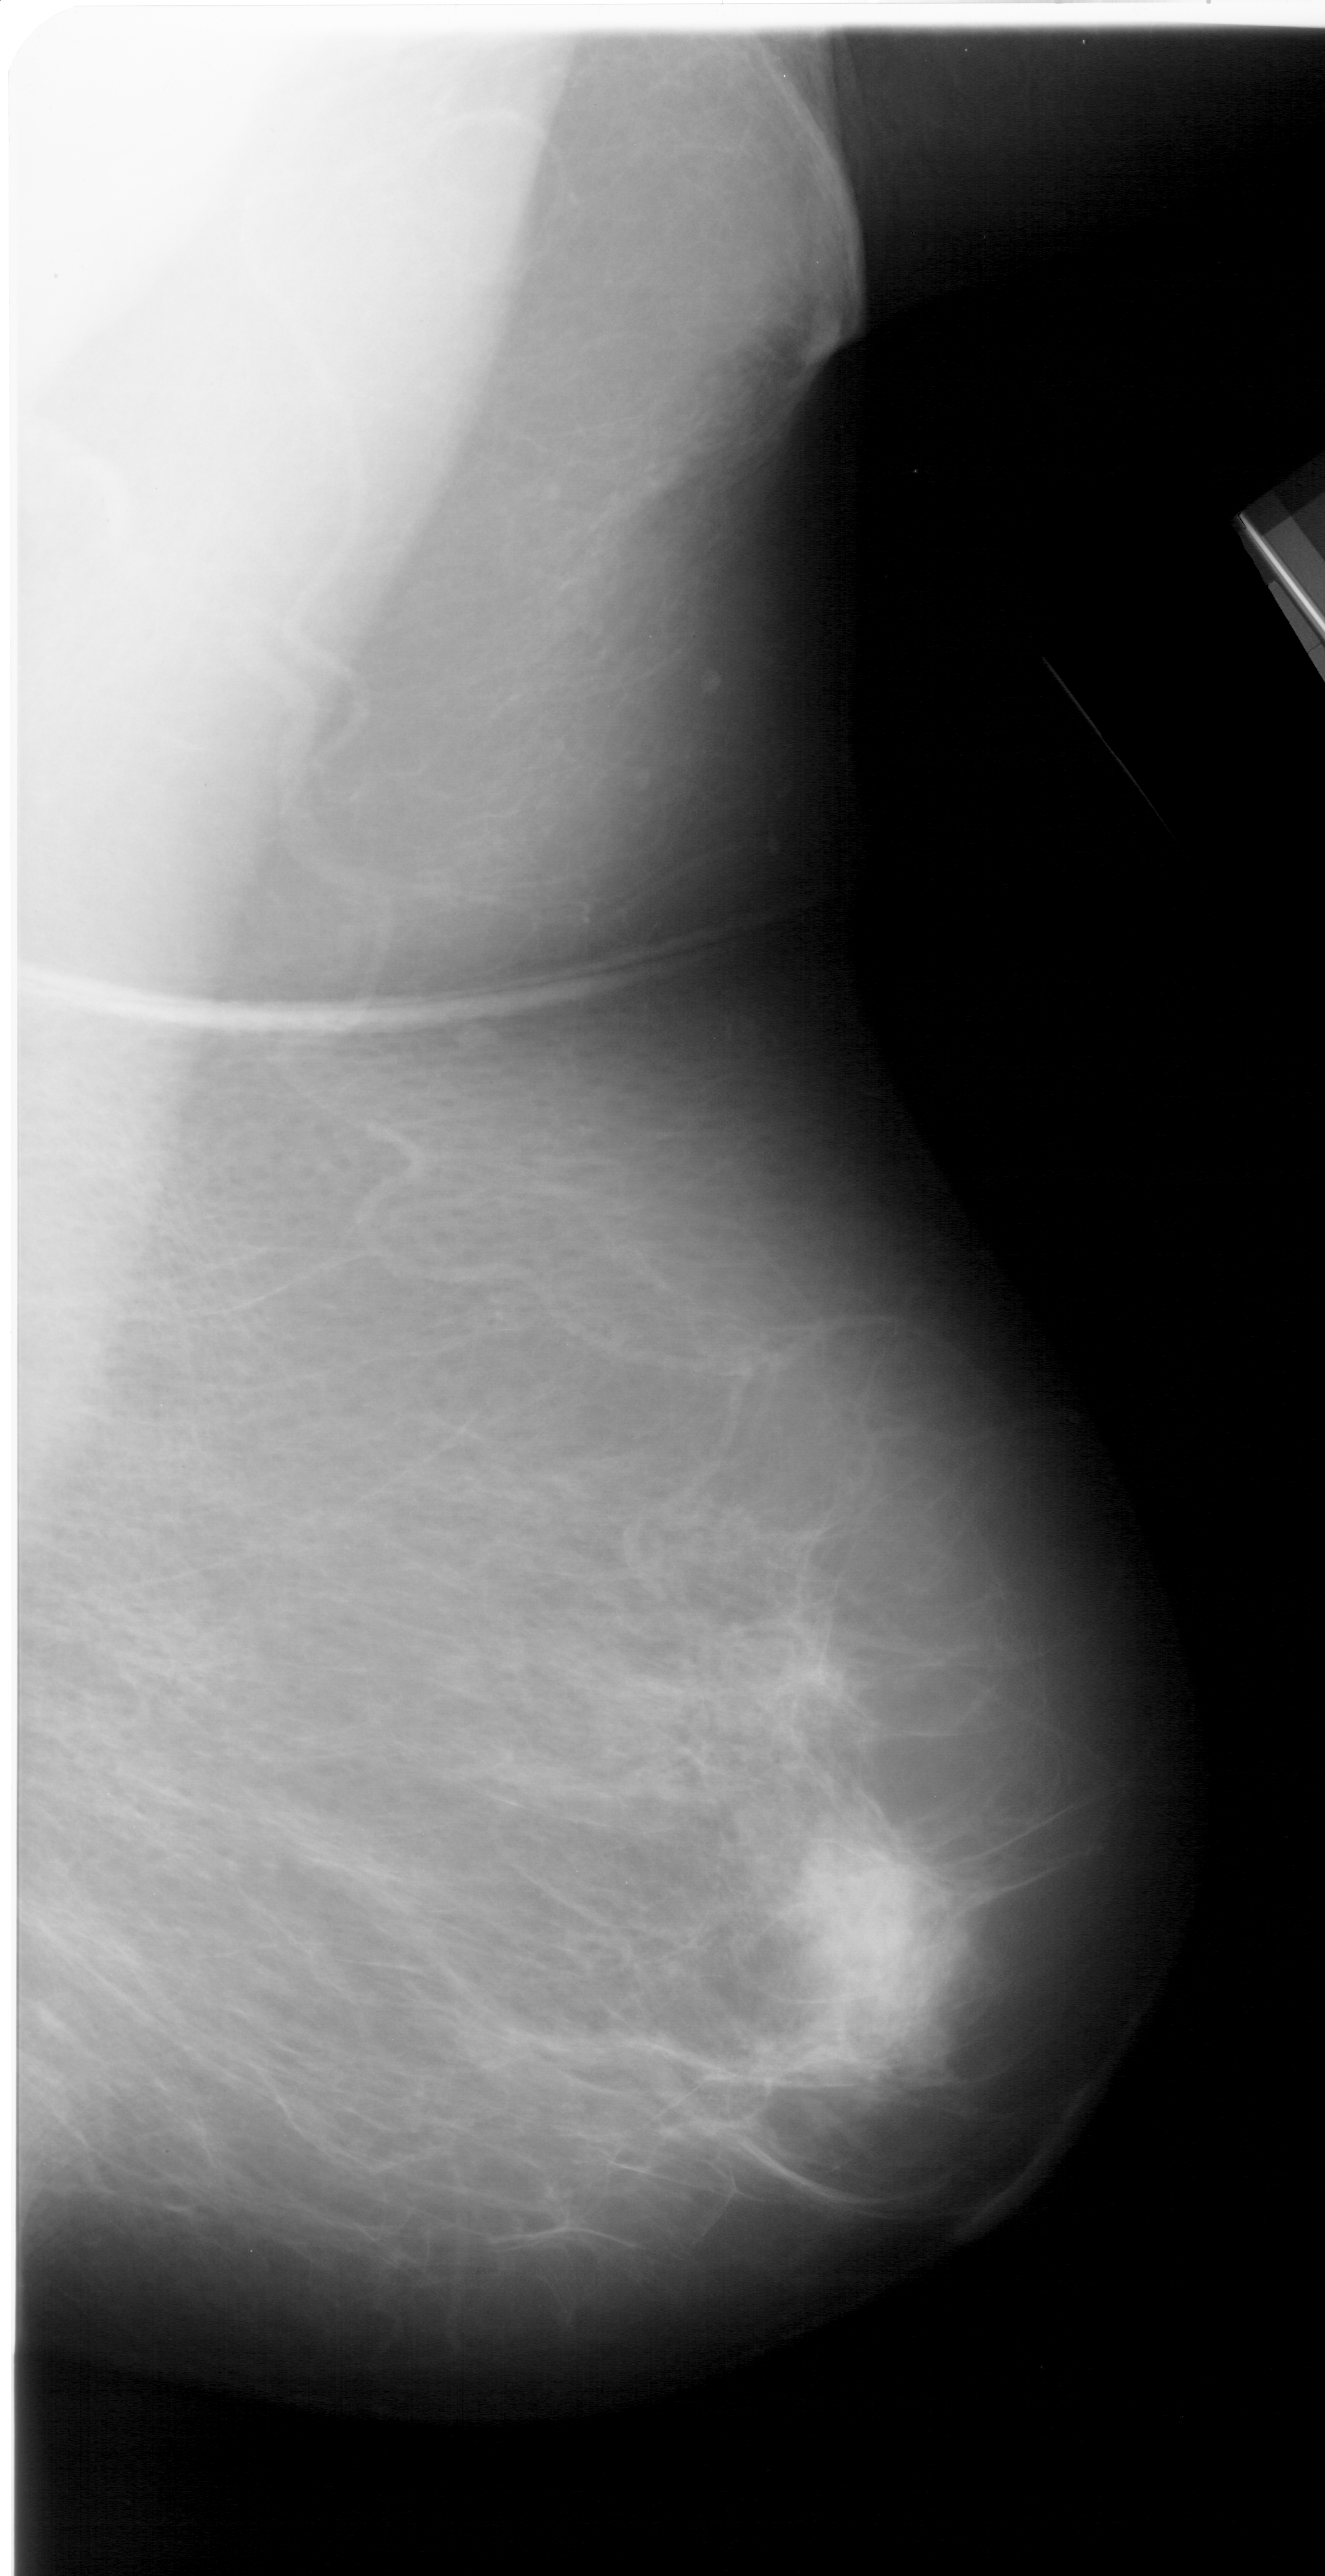
Mammogram (digitized film); right breast; mediolateral oblique (MLO) view.
- Marked findings (only marked abnormalities are described; nothing is implied about the rest of the image): mass, shape irregular, margins ill defined; BI-RADS assessment category 4; subtlety rating 4 on a 1 (subtle) to 5 (obvious) scale; pathology (as recorded): benign.